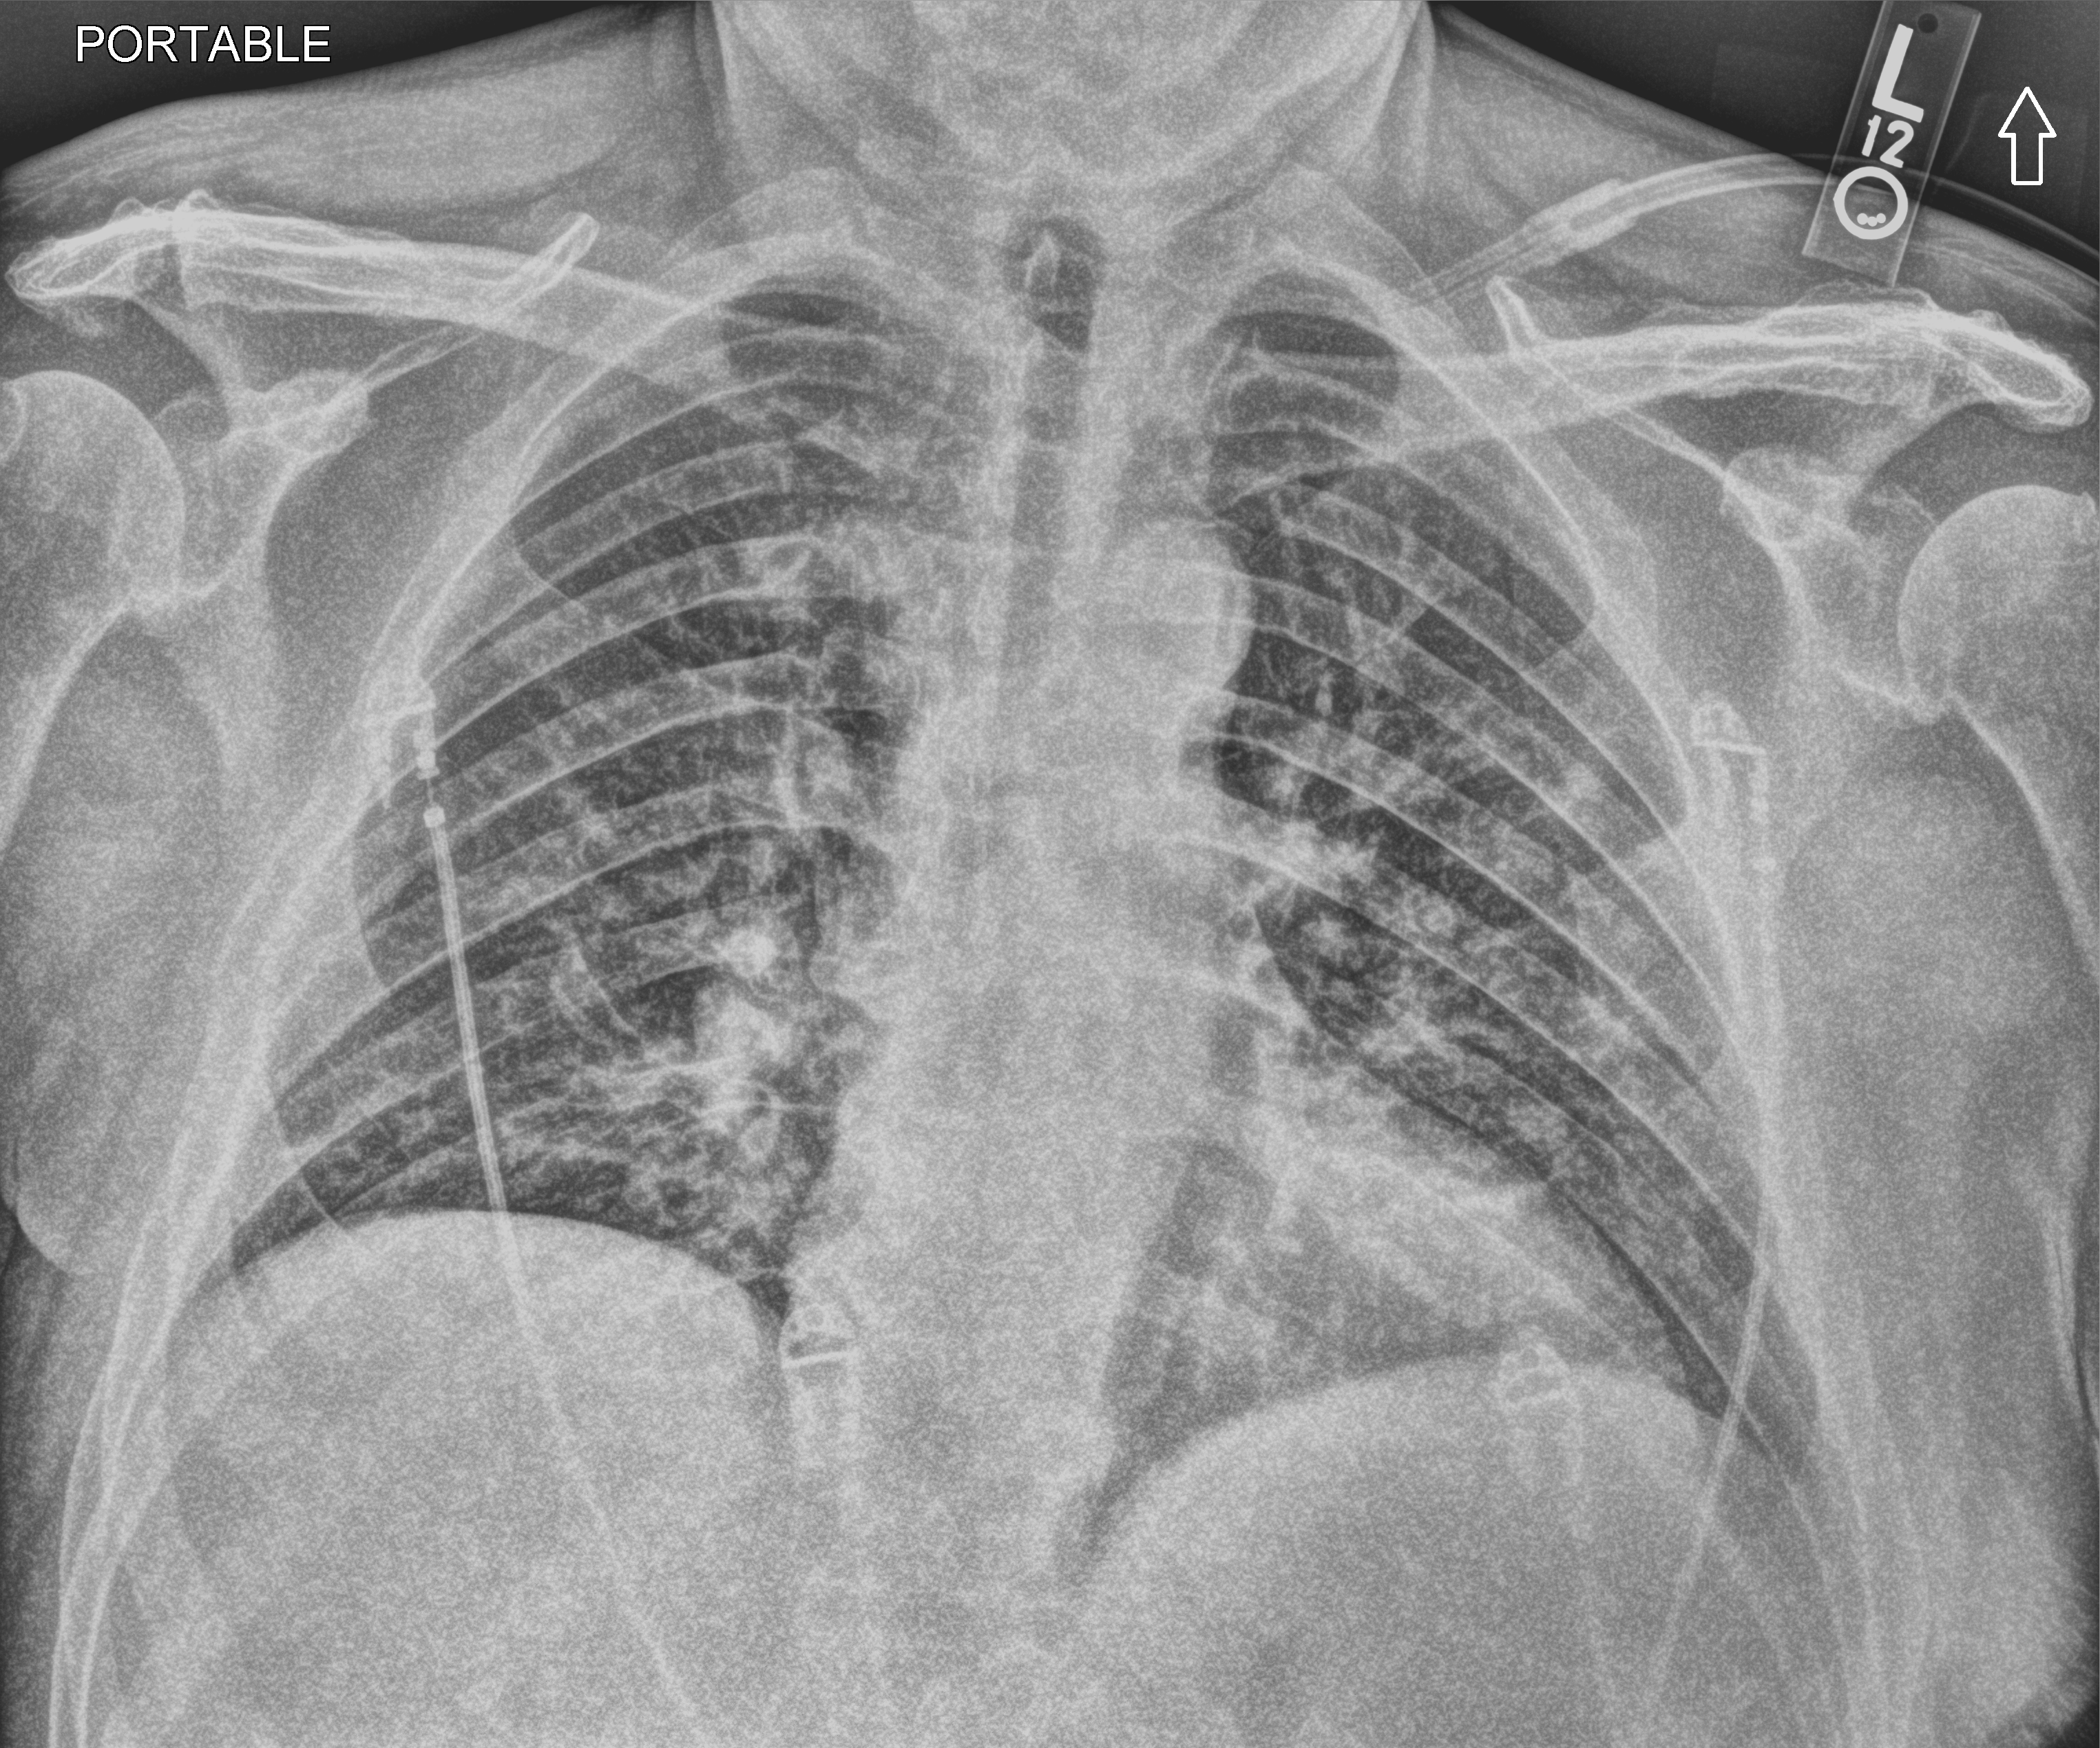
Bedside chest radiograph (computed radiography); anteroposterior (AP) projection. Male patient hospitalised with COVID-19, age 60–74 years.
From the hospital-stay record, not from the radiograph (when in the stay this image was taken is not recorded):
- admitted to intensive care during this hospital stay: no
- diabetes (admission record): yes
- mechanically ventilated during this hospital stay: no